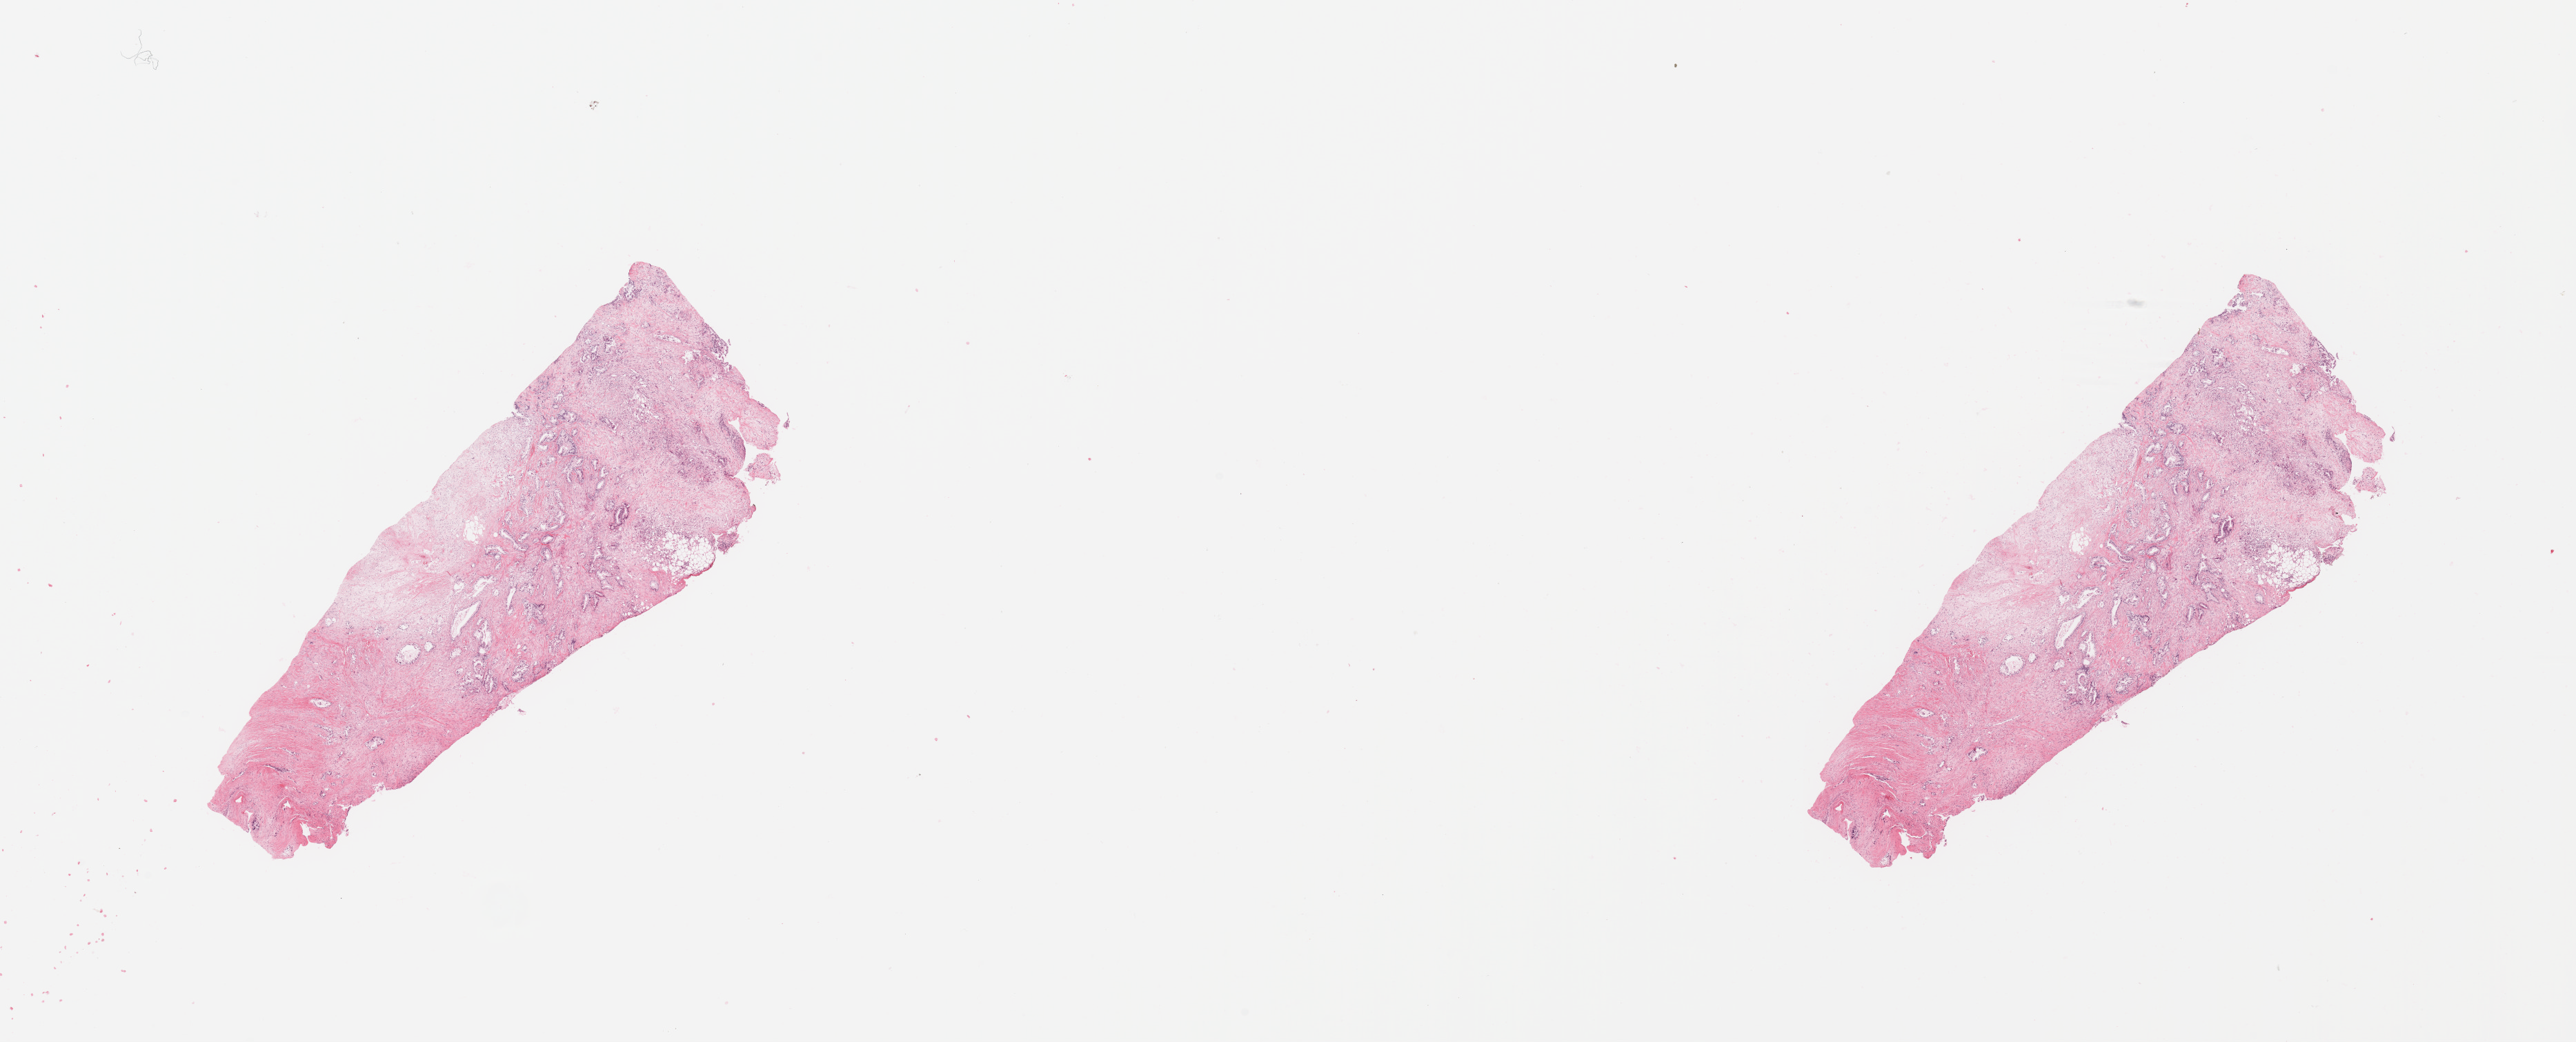
H&E-stained whole-slide image, whole scanned area (about 29.5 x 12.0 mm) shown as a low-resolution overview; pancreas, tumour tissue. Patient: female, age 78 years. Histologic grade: G1 (well differentiated).
Diagnosis: Infiltrating duct carcinoma, NOS. AJCC pathologic stage: III. Primary tumour site (as recorded): tail.